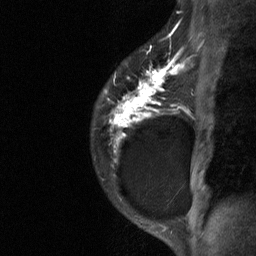
Breast MRI (dynamic contrast-enhanced), one sagittal slice; position 49 of 64 along the scan axis; dynamic contrast-enhanced study with each time point stored as its own series, time point 2 of 3 at this slice position (early post-contrast, ordered by acquisition time); 1.5 T; TE 4.8 ms, TR 27 ms; 2 mm slice thickness; 256 × 256 image matrix. Female patient, age 34 years. From the clinical record (not read from this slice): setting: breast cancer imaged before/during neoadjuvant chemotherapy; receptor status: HR-positive, HER2-negative.
Structures marked on this image (semi-automatic segmentation, software-assisted and operator-edited):
- analysis volume of interest (the breast-tissue region the enhancement analysis was run in; not a lesion): bounding box [x1, y1, x2, y2] px = [91, 44, 181, 191]
- tumour enhancement mask (voxels above the 90 % enhancement threshold inside the analysis volume of interest): [109, 46, 181, 147]